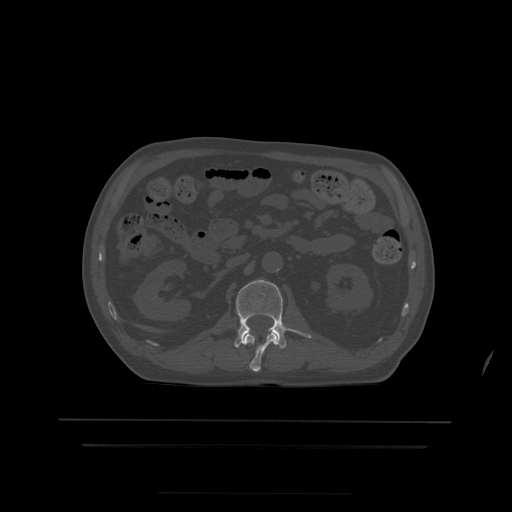
CT including the spine, one axial slice. Slice 154 of 522 in the series (ordered by position). Bone window (W 1800 / L 400 HU). 1.25 mm slice thickness. 512 × 512 image matrix, field of view 436 × 436 mm. Patient age 68 years. Case-level facts recorded for this patient, not image findings: primary cancer: urothelial.
Annotated regions visible in this slice (semi-automatic segmentation, software-assisted and operator-edited):
- L1 vertebra: bounding box [x1, y1, x2, y2] px = [245, 333, 278, 372]
- L2 vertebra: [234, 280, 312, 349]